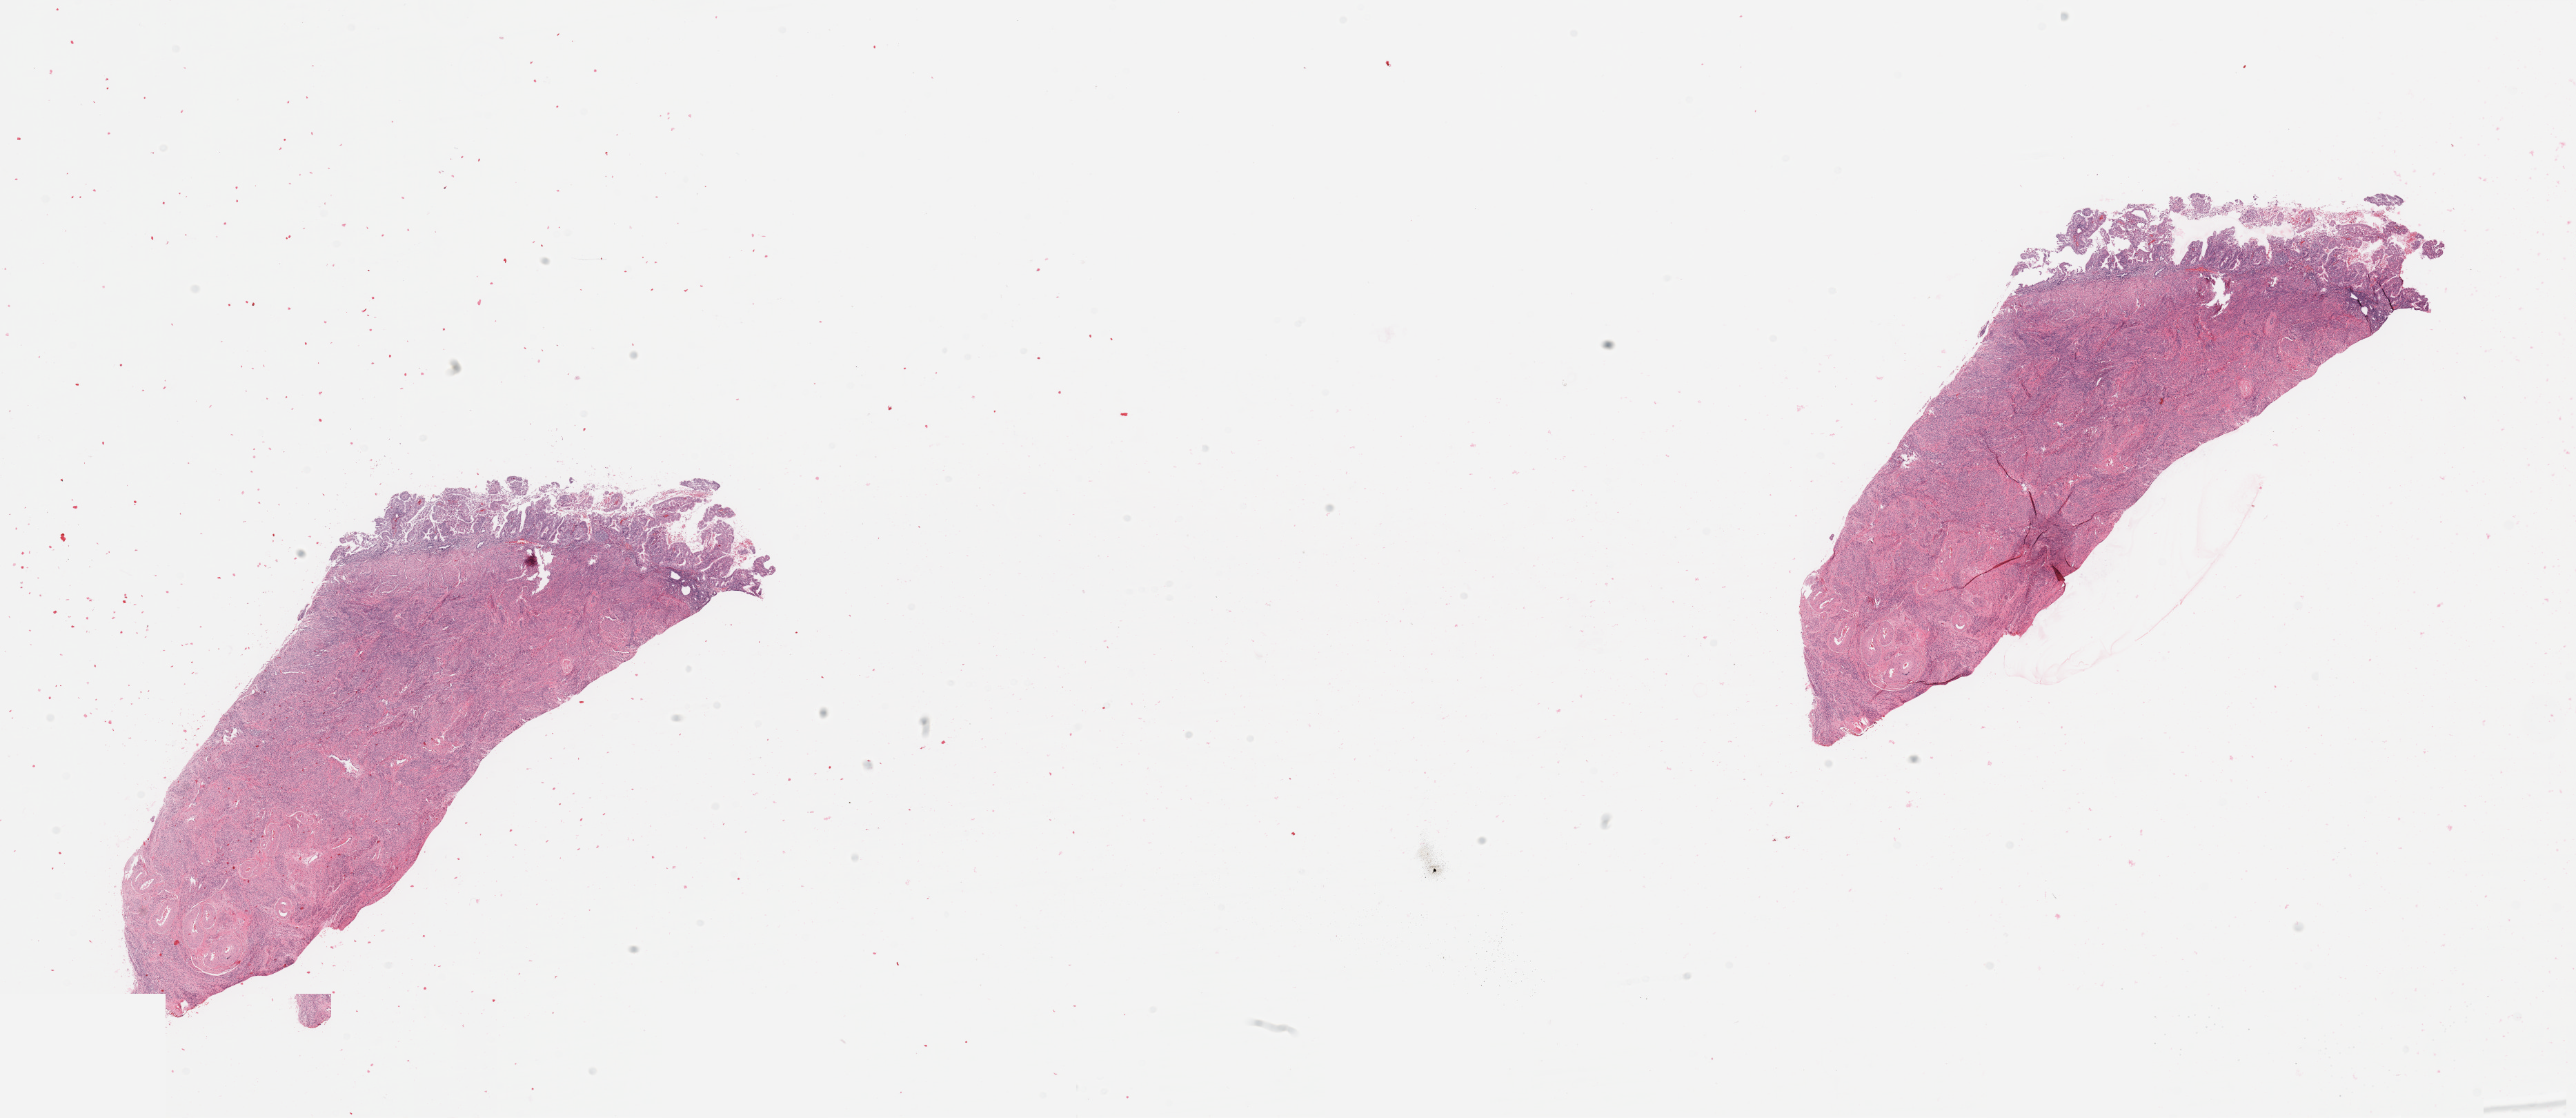
H&E whole-slide image, a low-resolution overview of the entire scanned area, about 29.5 x 12.8 mm, normal (non-tumour) tissue sample, uterus. Female, 74 y/o.
This section: normal (non-tumour) tissue from the same patient. Patient diagnosis: Endometrioid adenocarcinoma, NOS.